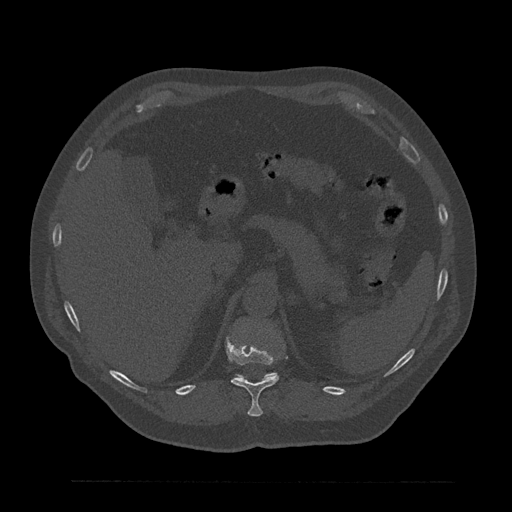
CT including the spine, one axial slice. Position 275 of 797 along the scan axis. 120 kVp. Bone window (W 1800 / L 400 HU). 0.5 mm slice thickness. 512 × 512 image matrix. Male patient, age 61 years. Case-level facts recorded for this patient, not image findings: primary cancer: prostate.
Annotated regions visible in this slice (semi-automatically segmented with operator editing):
- T11 vertebra: bounding box [x1, y1, x2, y2] px = [226, 337, 281, 417]
- T12 vertebra: [240, 373, 276, 377]